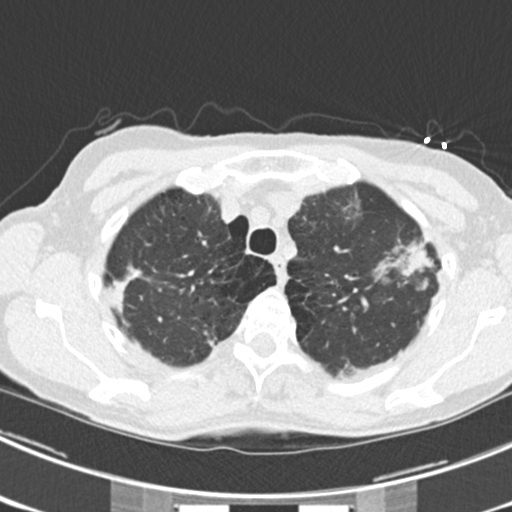
Low-dose screening chest CT, one axial slice; slice 180 of 225 in the series (ordered by position); lung window (W 1500 / L -600 HU); 2 mm slice thickness; 512 × 512 image matrix, field of view 302 × 302 mm.
Structures marked on this image (manually delineated by an expert):
- lesion 1 (tumor, upper lobe of left lung): bounding box (x1, y1, x2, y2) in pixels: (401, 243, 435, 278)